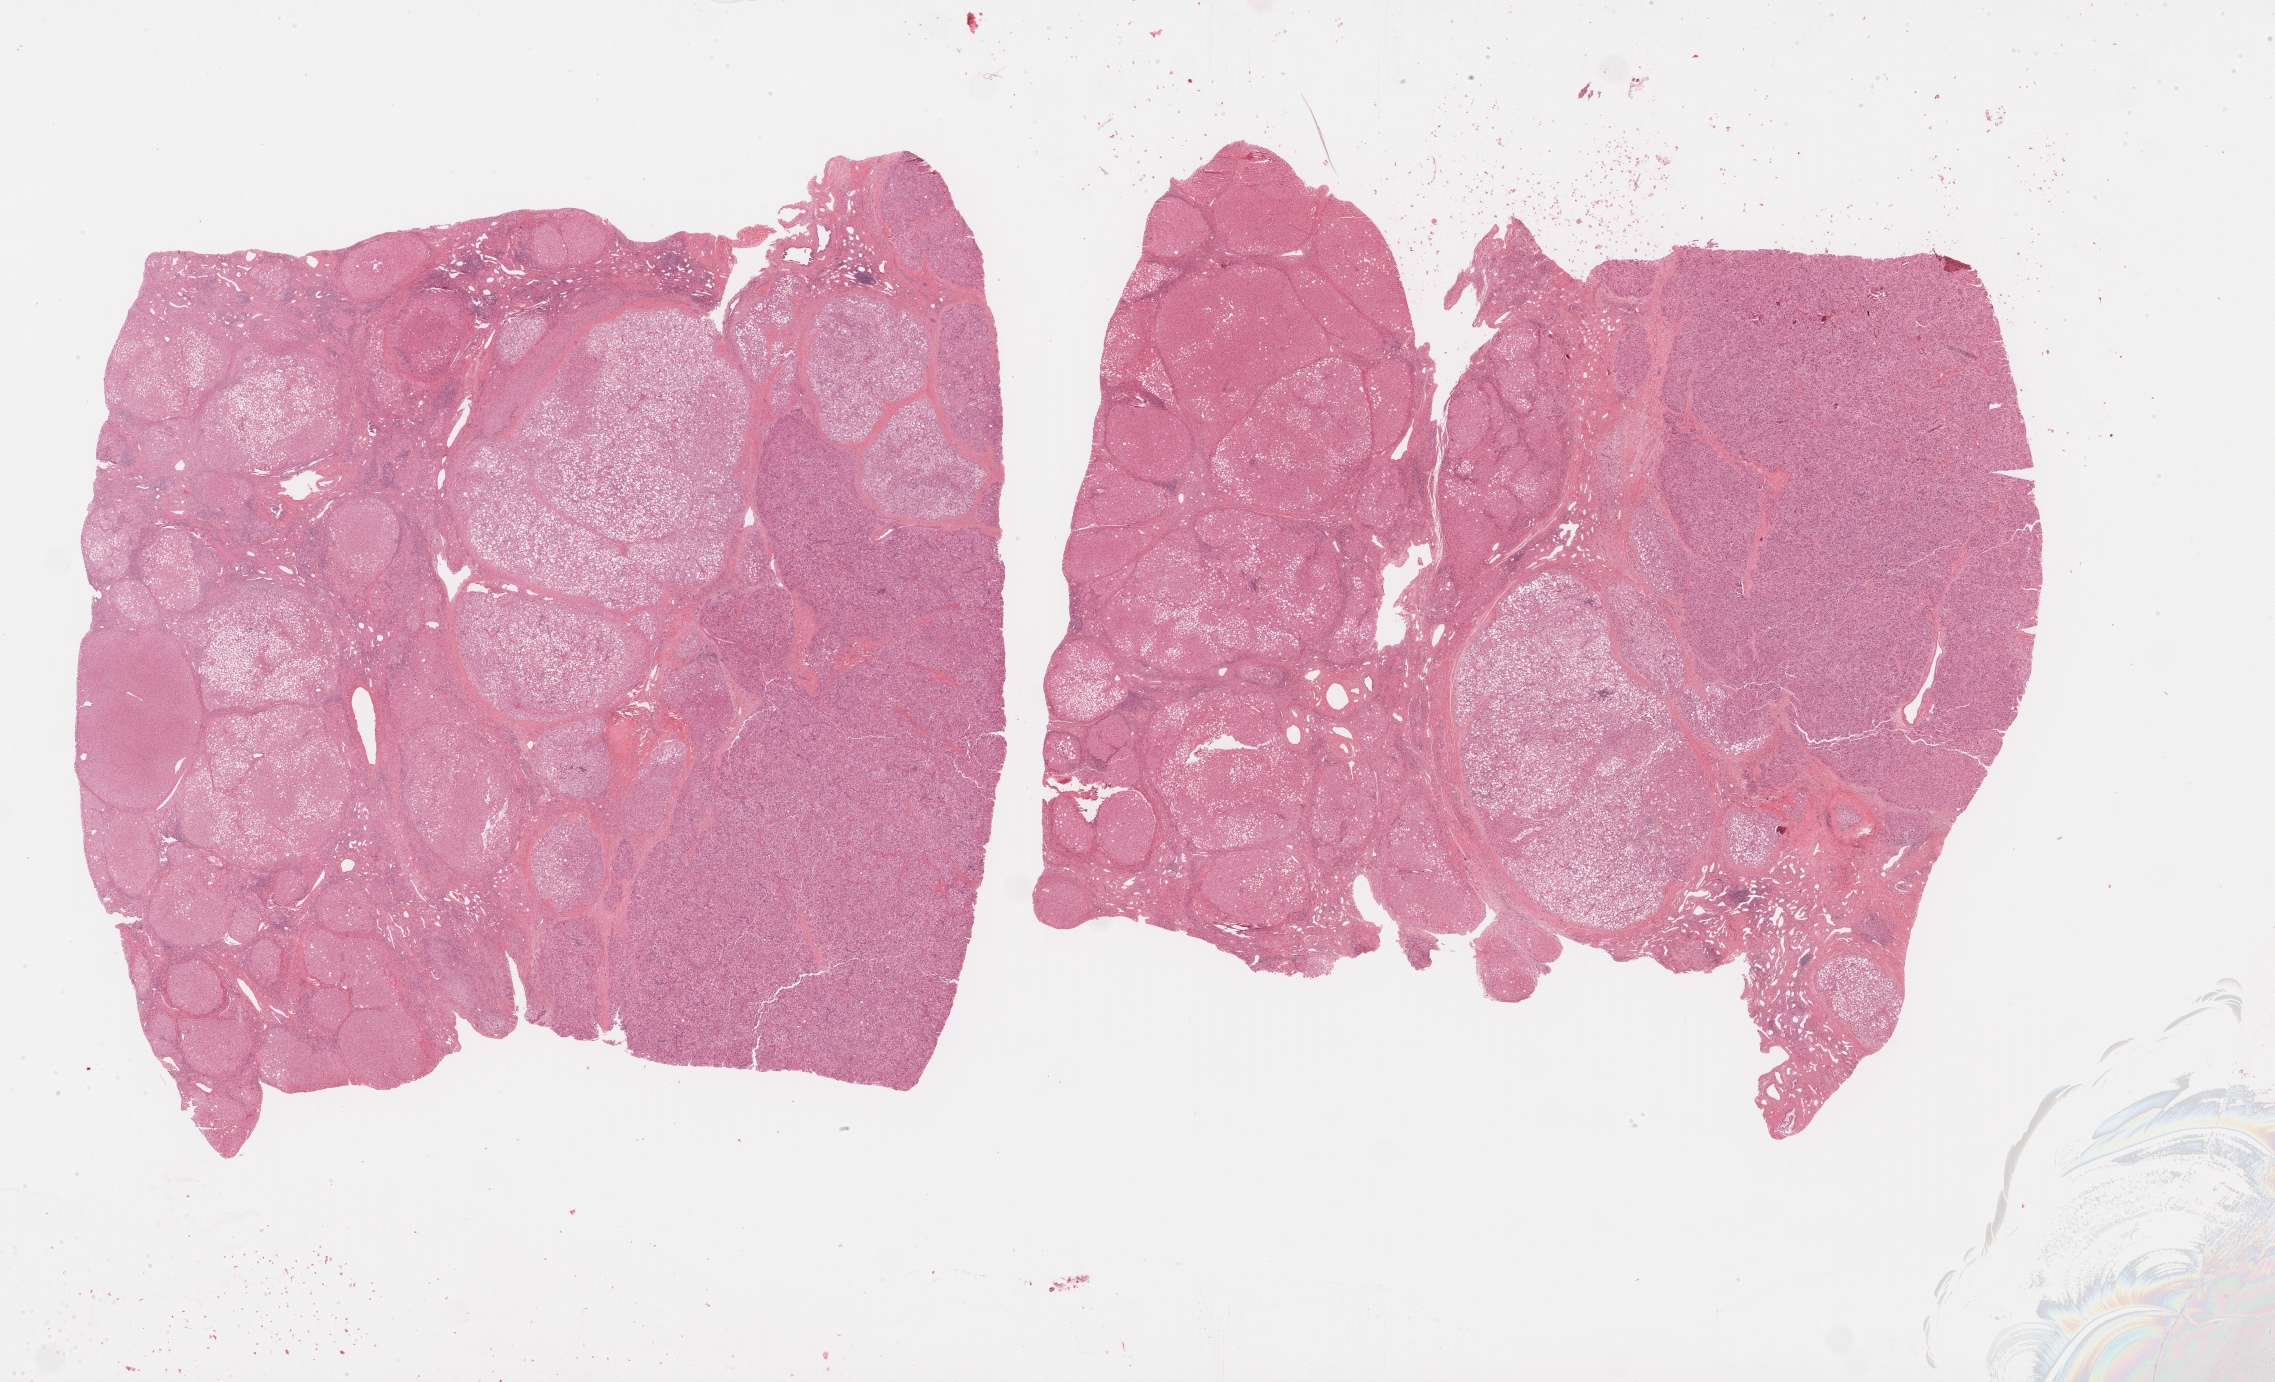
H&E whole-slide image, low-resolution overview of the scanned area, about 36.8 x 22.4 mm. Formalin-fixed paraffin-embedded (FFPE) diagnostic section. Primary tumour sample from the liver. Patient: male, age at initial diagnosis 70 years. Histologic grade: G2 (moderately differentiated).
- histologic diagnosis: Hepatocellular carcinoma, NOS
- AJCC pathologic stage: I (5th edition)